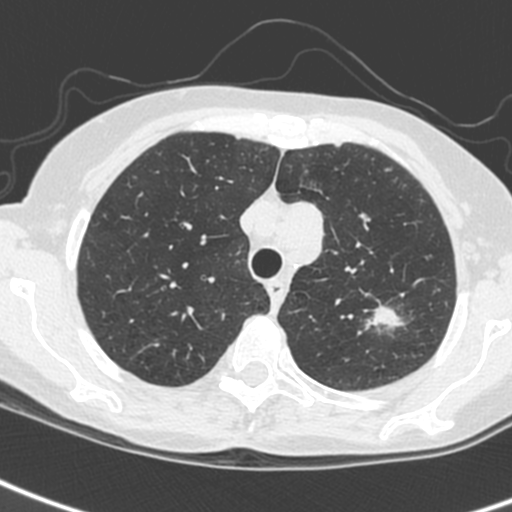
Low-dose screening chest CT, one axial slice; 120 kVp; lung window (W 1500 / L -600 HU); 512 × 512 image matrix.
Structures marked on this image (expert manual segmentation):
- lesion 1 (tumor, upper lobe of left lung): bounding box [x1, y1, x2, y2] px = [371, 307, 401, 327]
- lesion 3 (tumor, upper lobe of left lung): [295, 201, 324, 264]